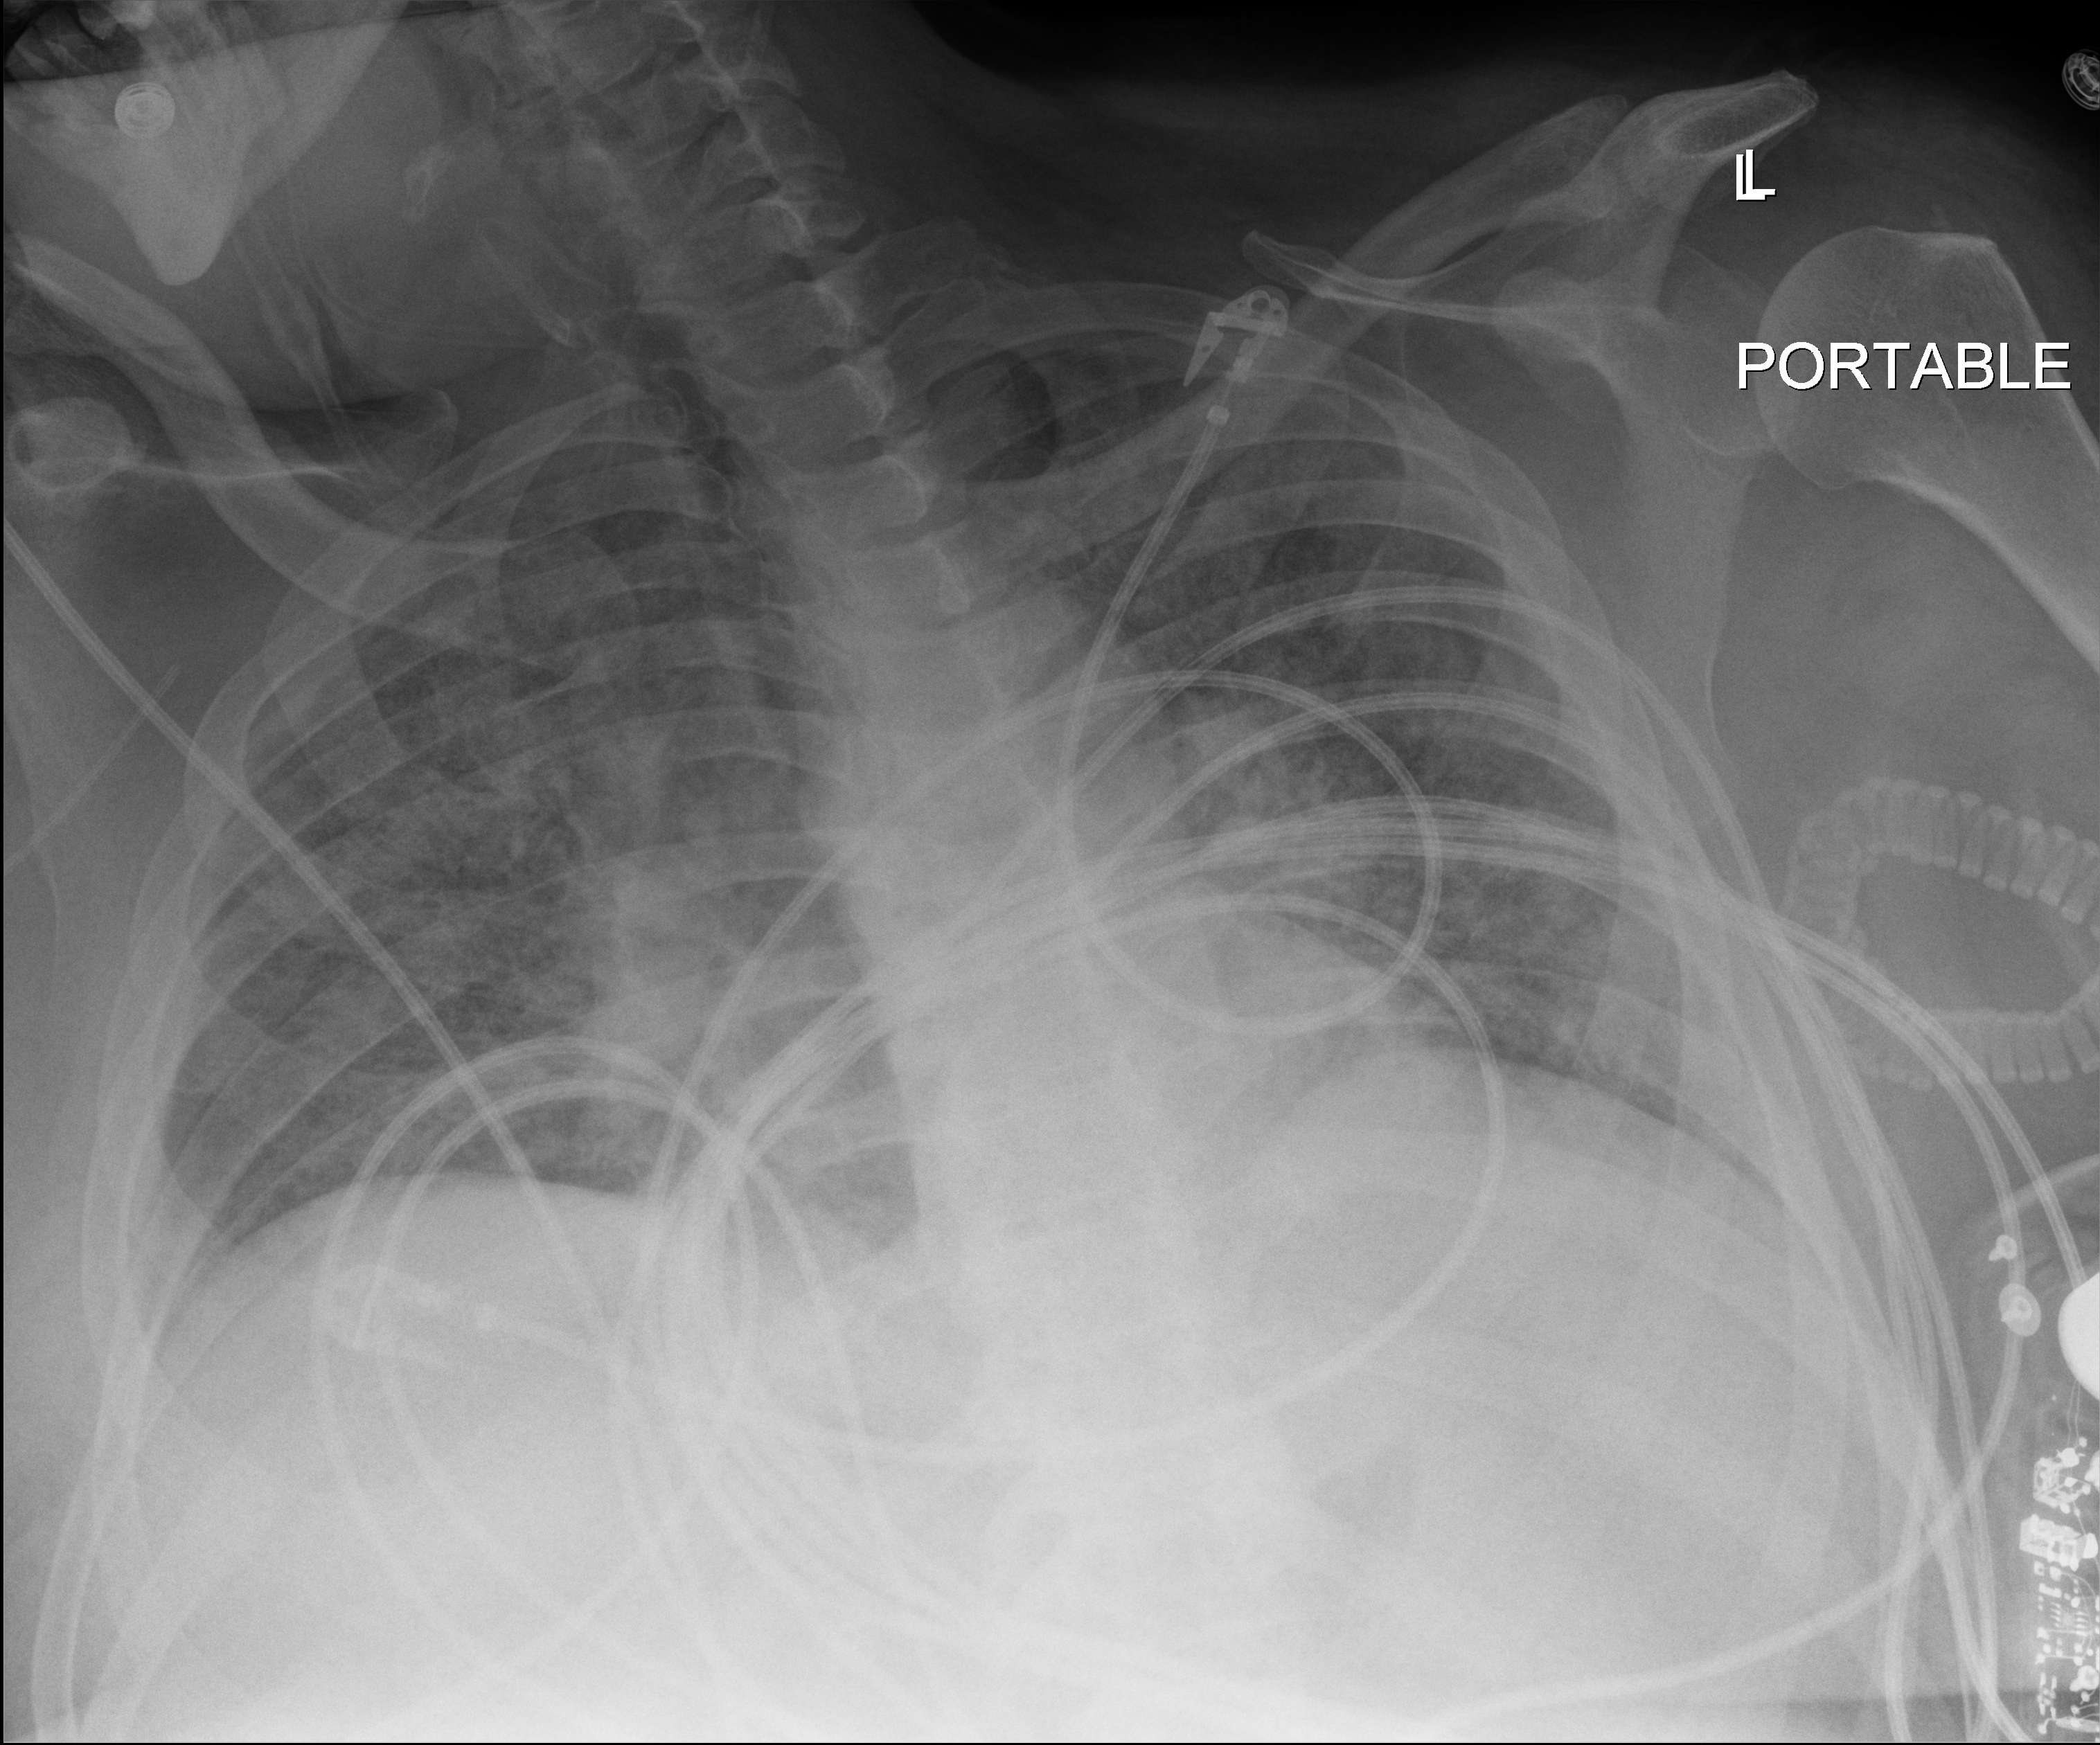
Portable chest radiograph, anteroposterior (AP) projection. Patient hospitalised with COVID-19; male, aged 60–74 years.
Hospital-stay facts (about this admission, not read from this image; timing relative to this image not recorded):
- length of hospital stay: 34 days
- chronic kidney disease (admission record): no
- smoking status (admission record): never